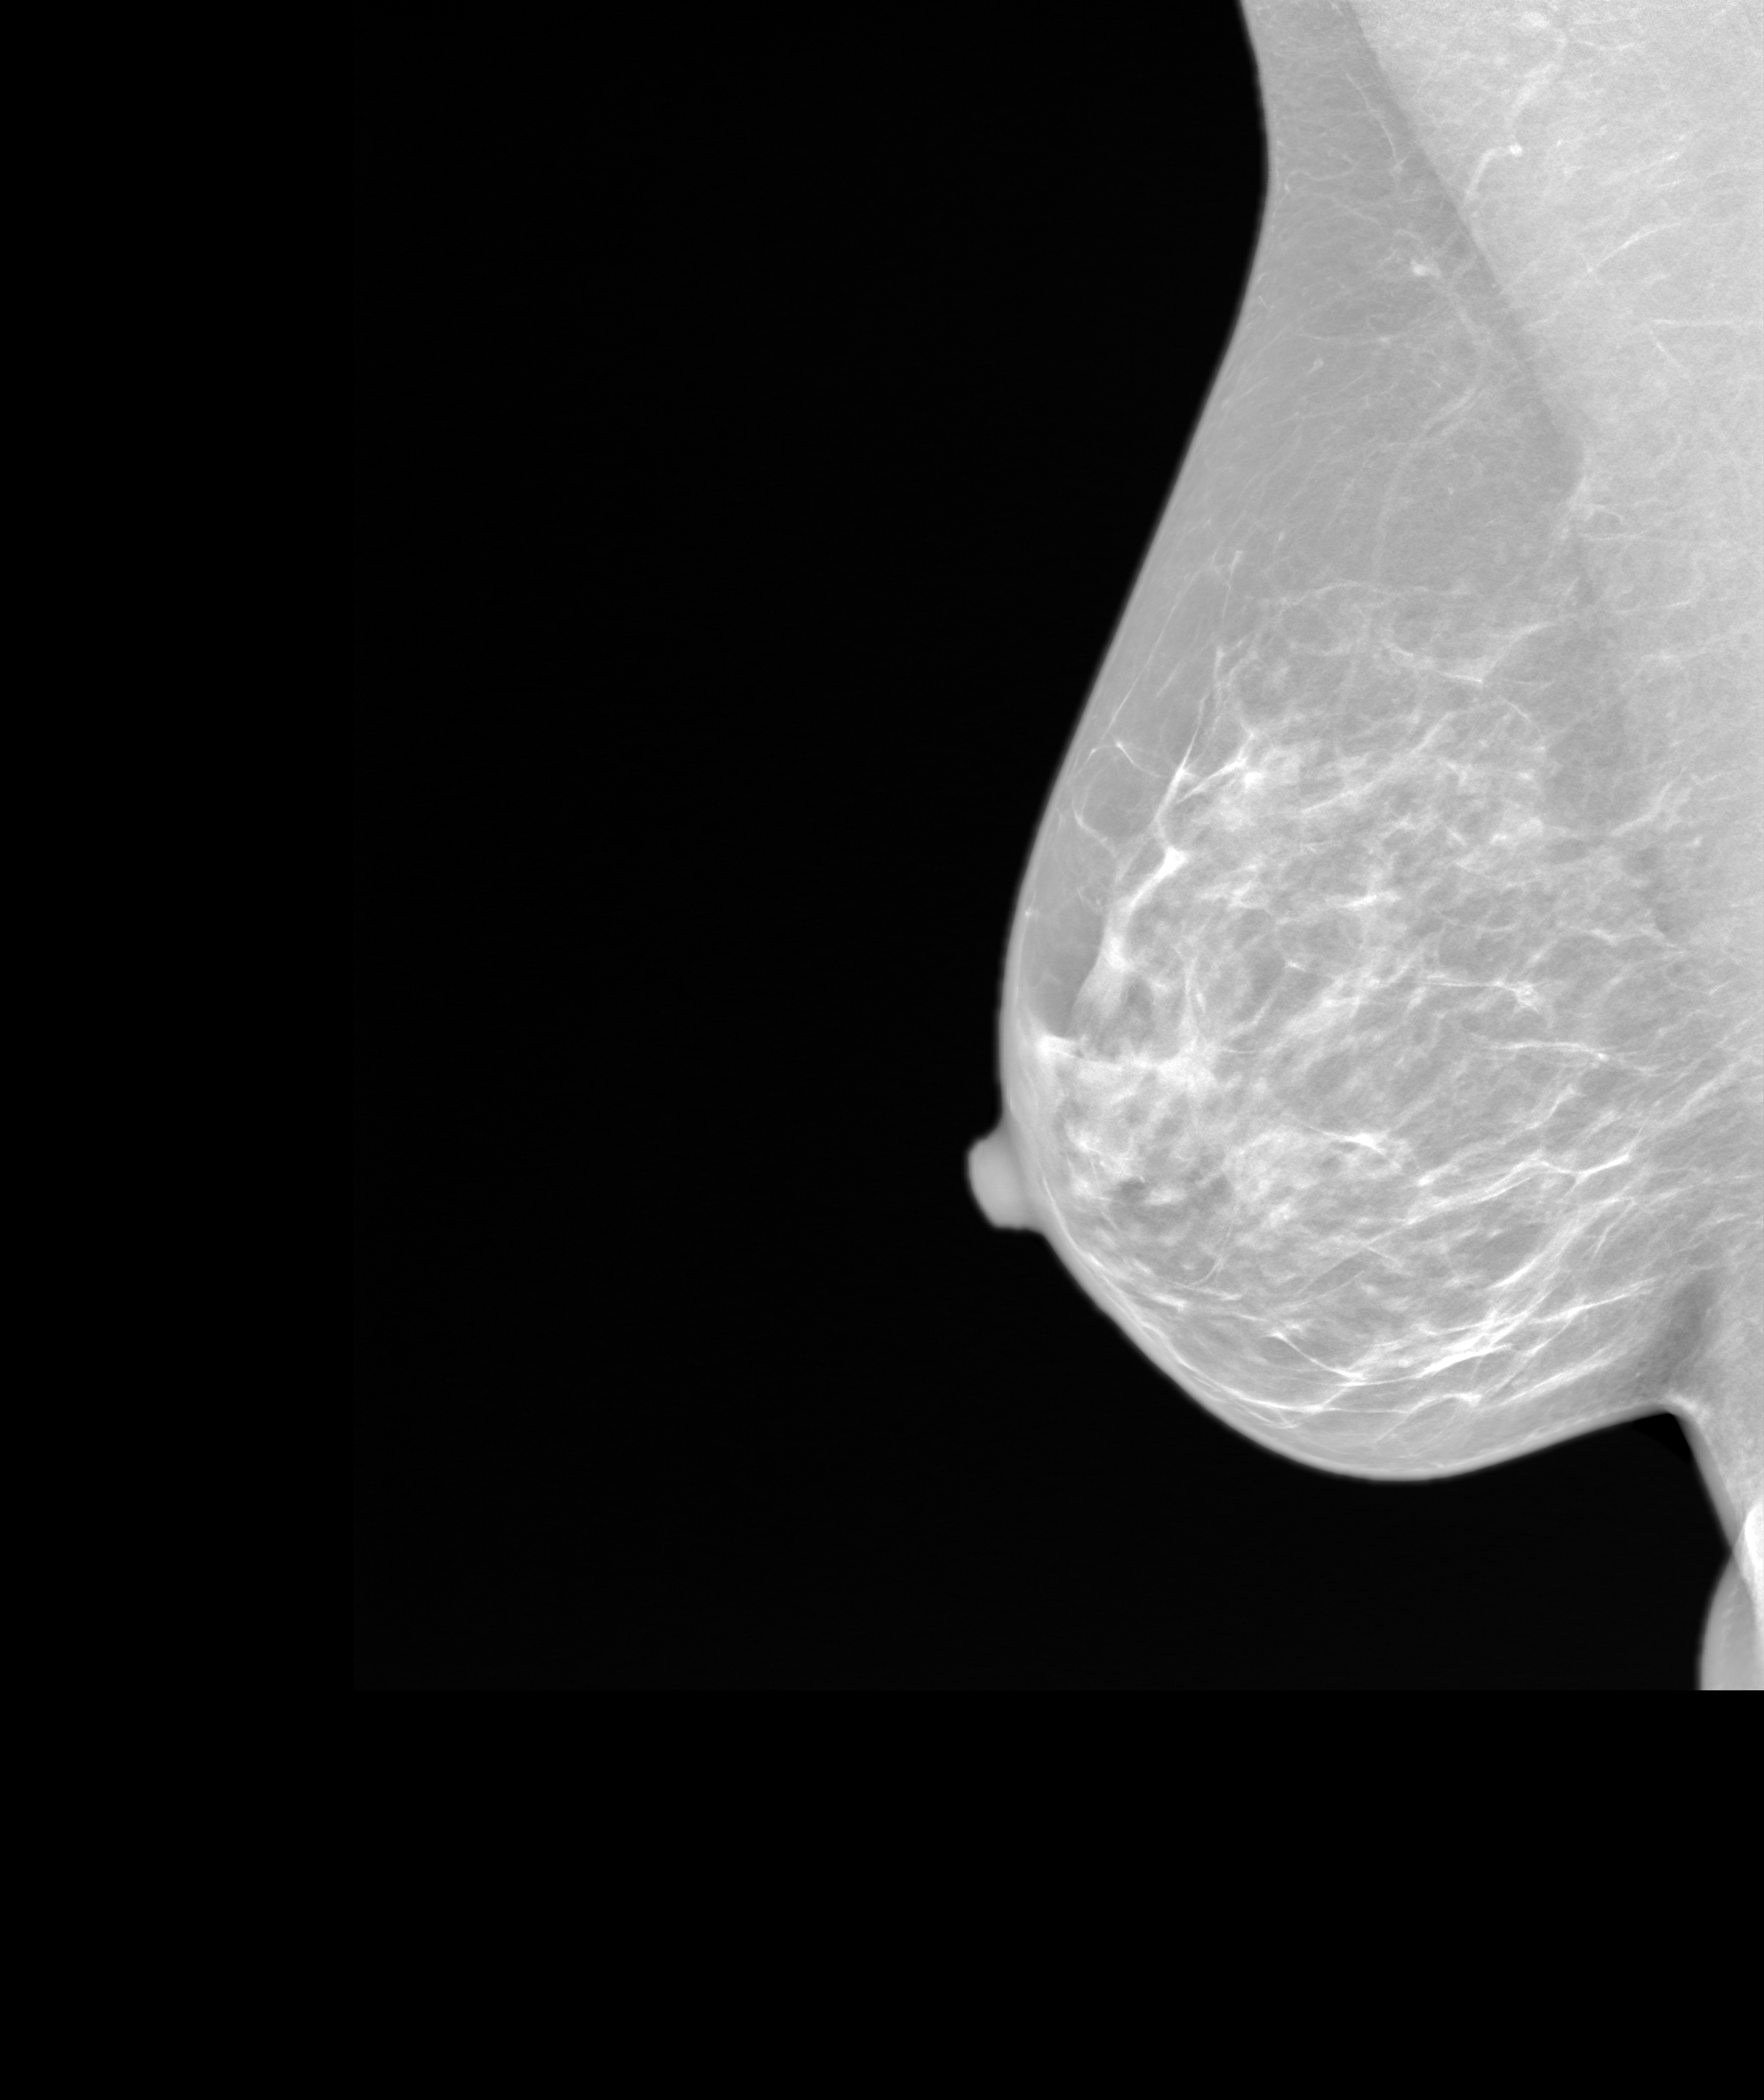
Screening examination. Patient aged 57 years (female).
Image type: synthesized 2-D view from tomosynthesis. Breast: right. Projection: medio-lateral oblique projection.